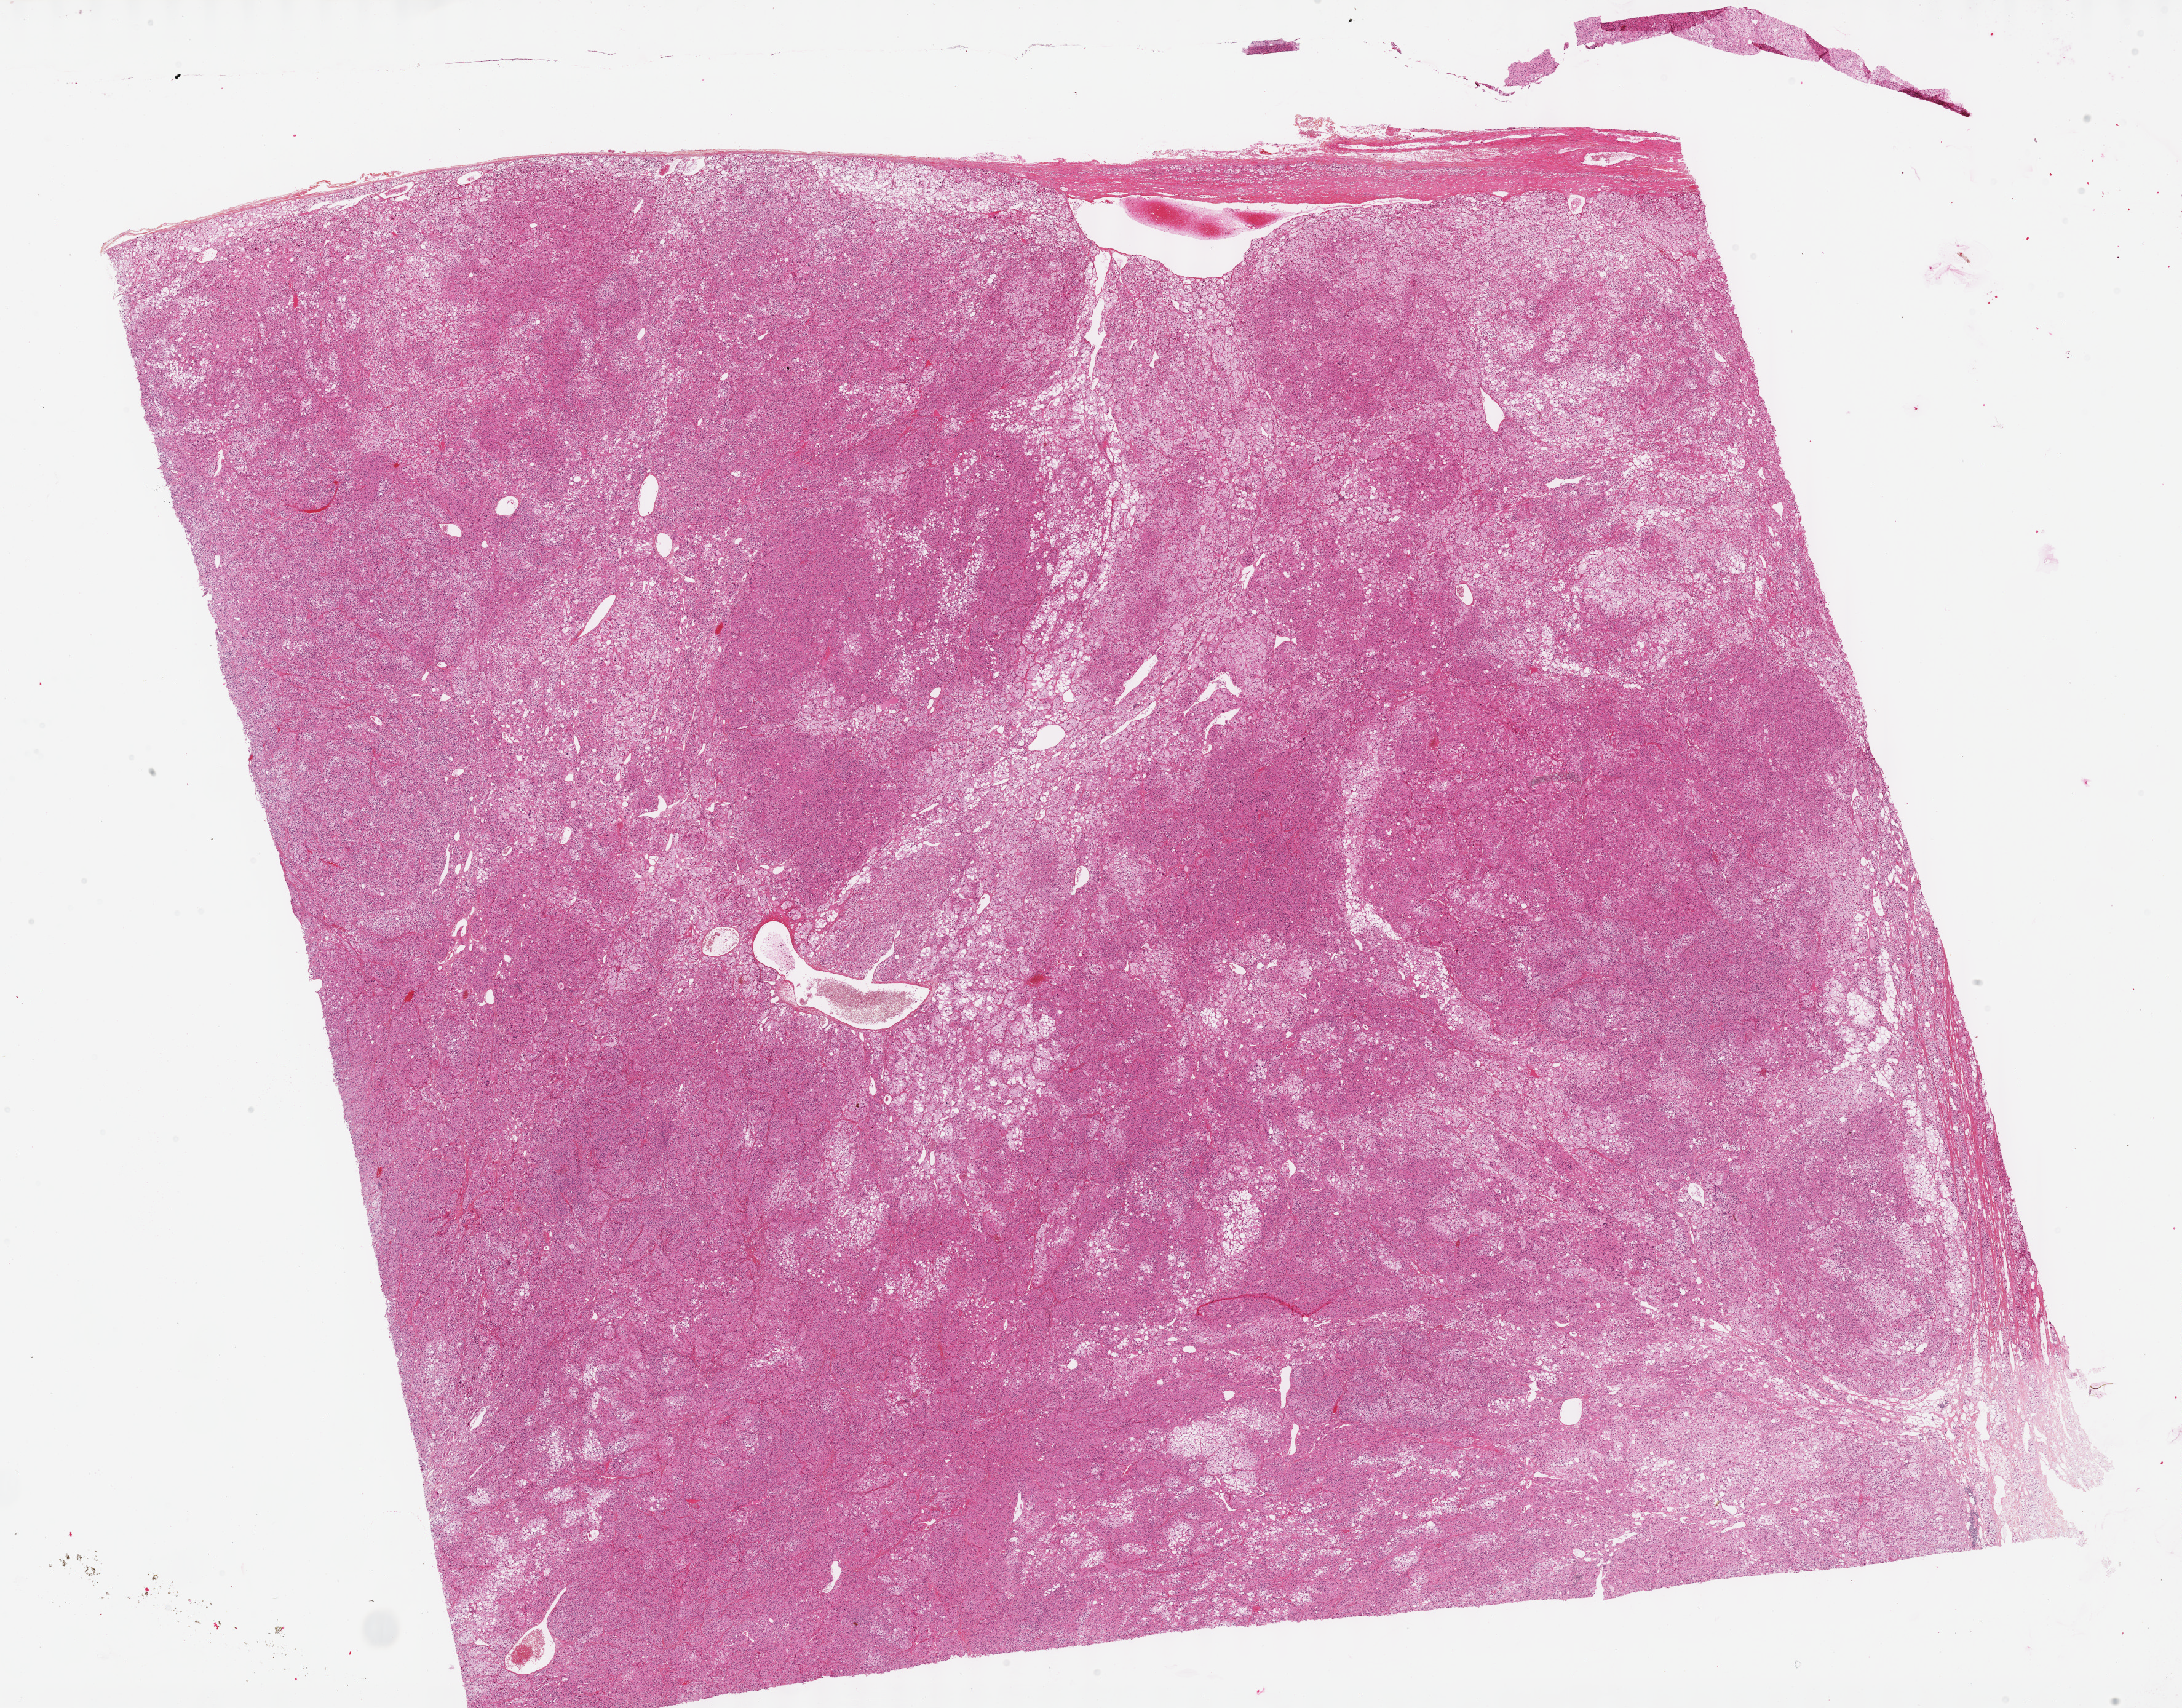
Digitized H&E-stained tissue section (whole slide) — a low-resolution overview of the entire scanned area, about 28.7 x 22.4 mm (slide scanned at 40x). FFPE section. Primary tumour sample from the adrenal cortex. Female, age 75 years at initial diagnosis.
• lymph nodes positive (case pathology): 0 of 10 examined
• pathologic diagnosis: Adrenal cortical carcinoma (cortex of adrenal gland)